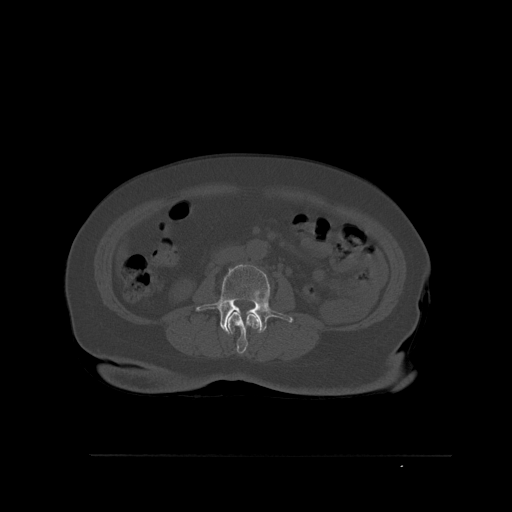
CT including the spine, one axial slice; position 232 of 527 along the scan axis; bone window (W 1800 / L 400 HU); 1.5 mm slice thickness; 512 × 512 image matrix, field of view 470 × 470 mm. Patient: female, 73 years. Case-level facts recorded for this patient, not image findings: primary cancer: breast; vertebrae with lytic lesions (as recorded): L2.
Outlined on this slice (semi-automatic segmentation, software-assisted and operator-edited):
- L2 vertebra: bounding box [x1, y1, x2, y2] px = [227, 311, 257, 354]
- L3 vertebra: [196, 264, 293, 335]
- L4 vertebra: [256, 319, 259, 329]